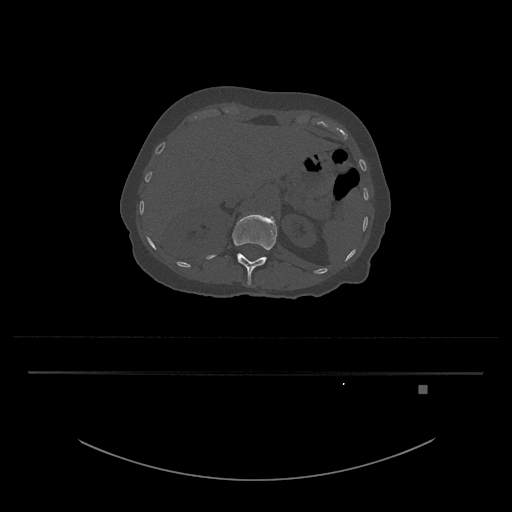
CT including the spine, one axial slice; slice 547 of 797 in the series (ordered by position); reconstruction kernel Br40s/3; 120 kVp; bone window (W 1800 / L 400 HU); 0.5 mm slice thickness; 512 × 512 image matrix. Patient: female, 57 years. Case-level facts recorded for this patient, not image findings: primary cancer: cervical.
Outlined on this slice (semi-automatically segmented with operator editing):
- L1 vertebra: bounding box (x1, y1, x2, y2) in pixels: (206, 214, 278, 285)